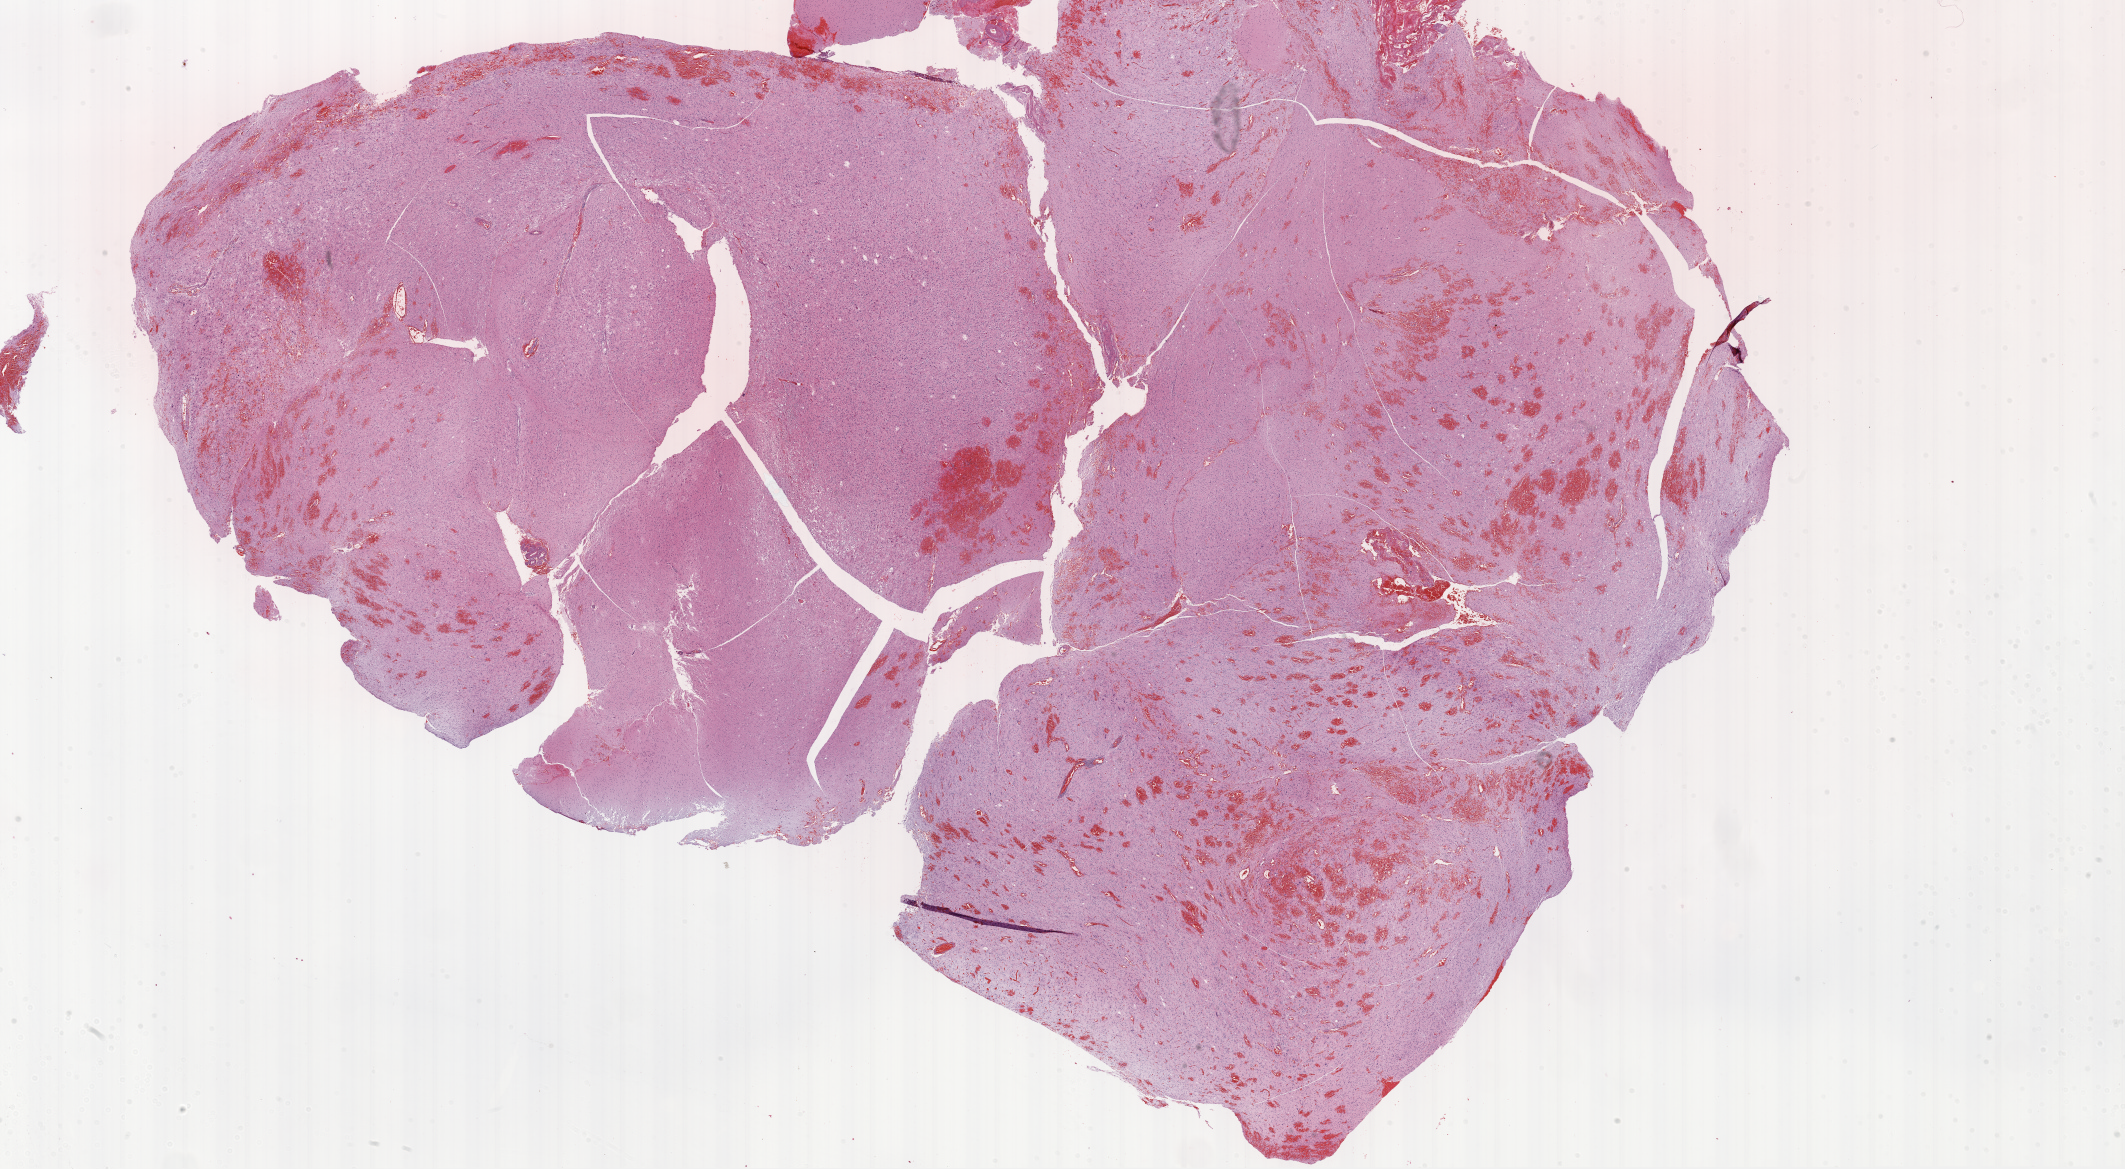
Hematoxylin and eosin (H&E) stained whole-slide image, whole scanned area (about 34.1 x 18.8 mm, acquisition: 20x scan) shown as a low-resolution overview, formalin-fixed paraffin-embedded (FFPE) diagnostic section, primary tumour sample from the brain. Patient: male, age at initial diagnosis 58 years.
- diagnosis: Glioblastoma